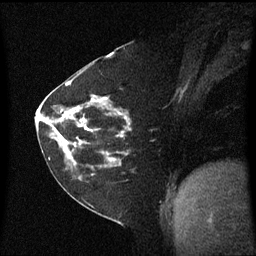
Breast MRI (dynamic contrast-enhanced), one sagittal slice. Position 30 of 60 along the scan axis. Dynamic contrast-enhanced series, image 2 of 3 at this slice position (ordered by acquisition). 1.5 T. TE 4.2 ms, TR 8.4 ms. 2 mm slice thickness. 256 × 256 image matrix, field of view 210 × 210 mm. Female patient, age 60 years. From the clinical record (not read from this slice): setting: breast cancer imaged before/during neoadjuvant chemotherapy; receptor status: triple-negative.
Outlined on this slice (semi-automatic segmentation, software-assisted and operator-edited):
- analysis volume of interest (the breast-tissue region the enhancement analysis was run in; not a lesion): box from (x=45, y=99) to (x=133, y=182) px
- tumour enhancement mask (voxels above the 70 % enhancement threshold inside the analysis volume of interest): (x=49, y=99)–(x=123, y=163)